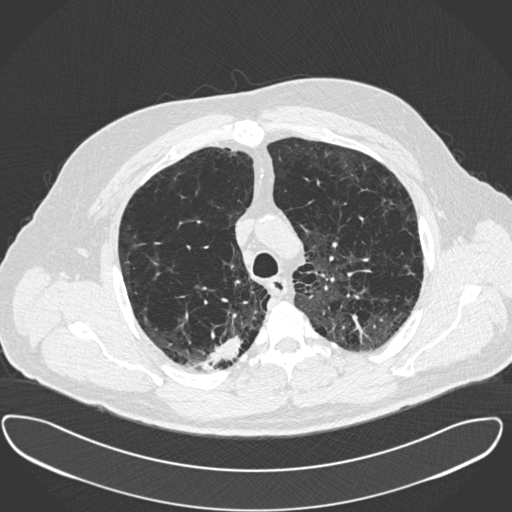
Low-dose screening chest CT, one axial slice. Slice 296 of 385 in the series (ordered by position). Reconstruction kernel B30f. 120 kVp. Lung window (W 1500 / L -600 HU). 512 × 512 image matrix, field of view 408 × 408 mm.
Annotated regions visible in this slice (manually delineated by an expert):
- lesion 1 (tumor, upper lobe of right lung): bounding box [x1, y1, x2, y2] px = [202, 336, 242, 370]